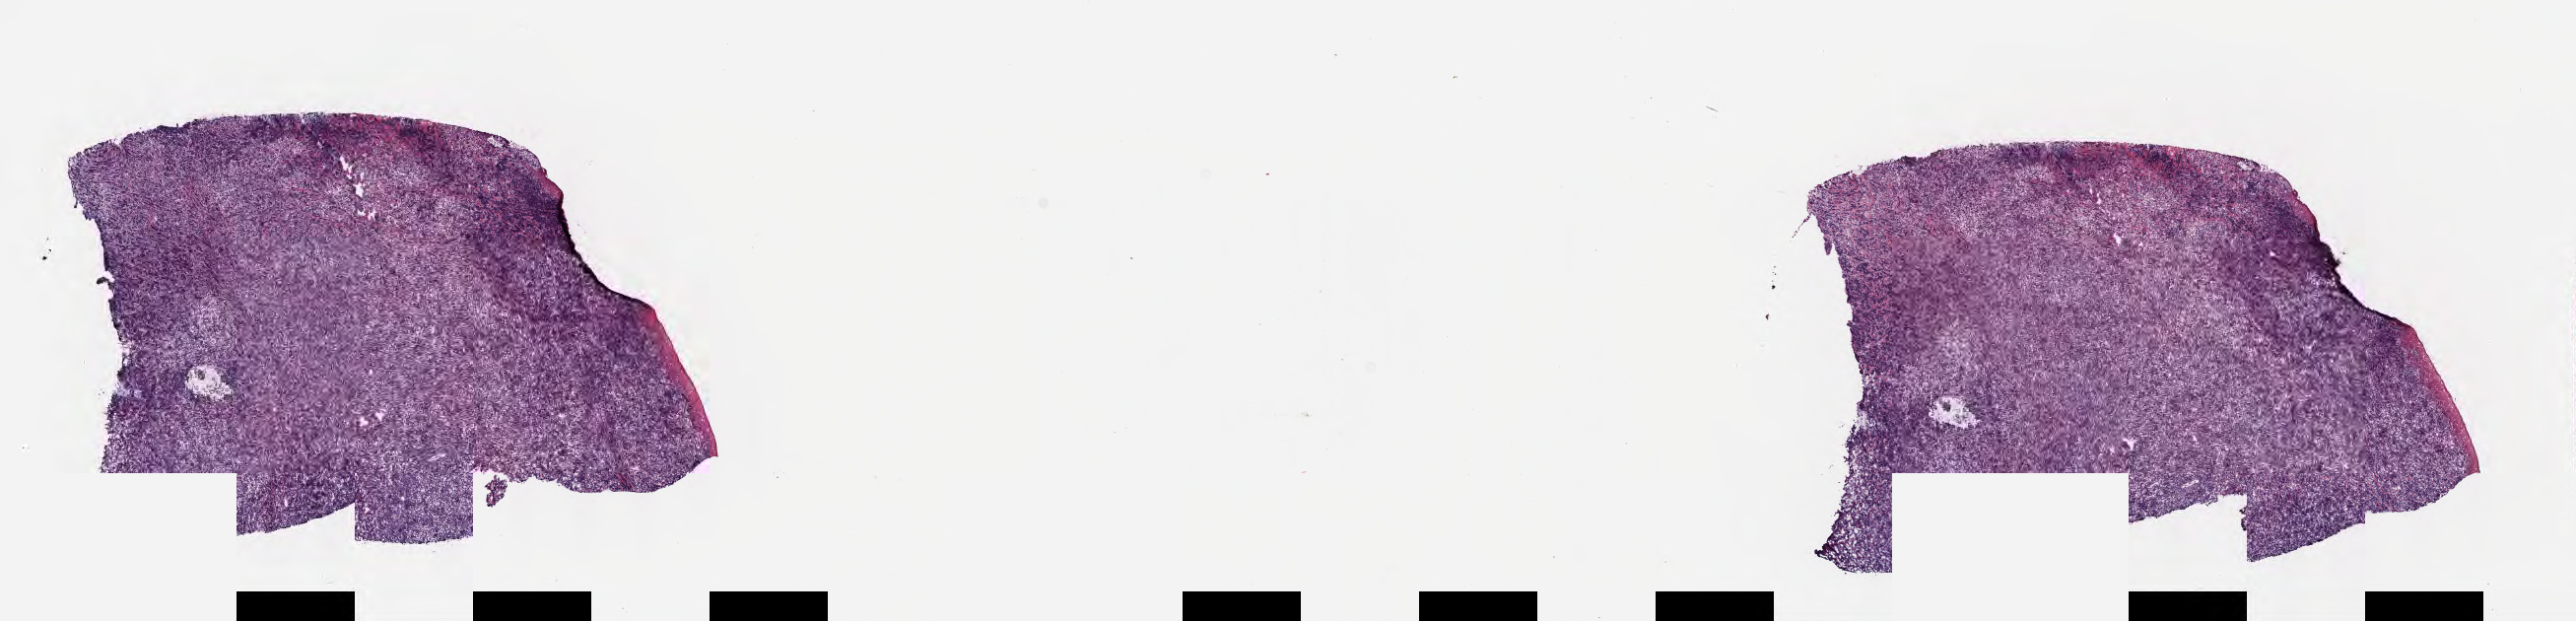
Whole-slide image, hematoxylin and eosin (H&E) stain, whole scanned area (about 21.1 x 5.1 mm) shown as a low-resolution overview, cryosection, primary tumor, anatomic site: cranium. Male patient, aged 13. Slide review estimates, as recorded: tumor cells 85%, tumor nuclei 90%, stromal cells 10%, necrosis 5%, normal cells 0%. Inflammatory infiltration, as recorded: lymphocyte infiltration 30%, monocyte infiltration 40%, neutrophil infiltration 0%.
Ann Arbor stage (patient): Stage III. Histologic diagnosis: Diffuse large B-cell lymphoma, NOS. Section: bottom of the tissue portion.